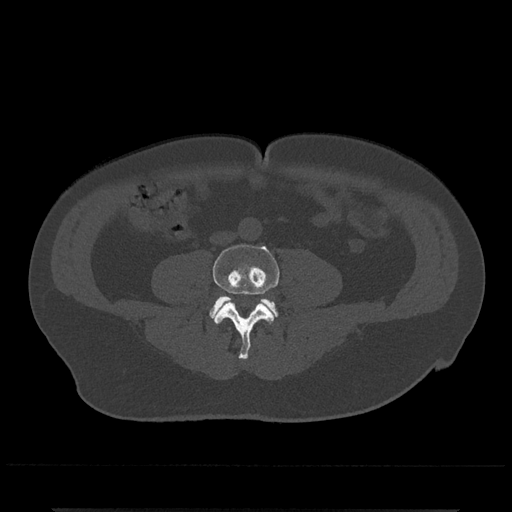
CT including the spine, one axial slice; slice 139 of 797 in the series (ordered by position); reconstruction kernel Br40s/3; 120 kVp; bone window (W 1800 / L 400 HU); 512 × 512 image matrix, field of view 393 × 393 mm. Patient: male, 67 years. From the clinical record (not read from this slice): primary cancer: prostate.
Outlined on this slice (semi-automatic segmentation, software-assisted and operator-edited):
- L4 vertebra: bounding box [x1, y1, x2, y2] px = [213, 244, 280, 360]
- L5 vertebra: [209, 295, 278, 319]